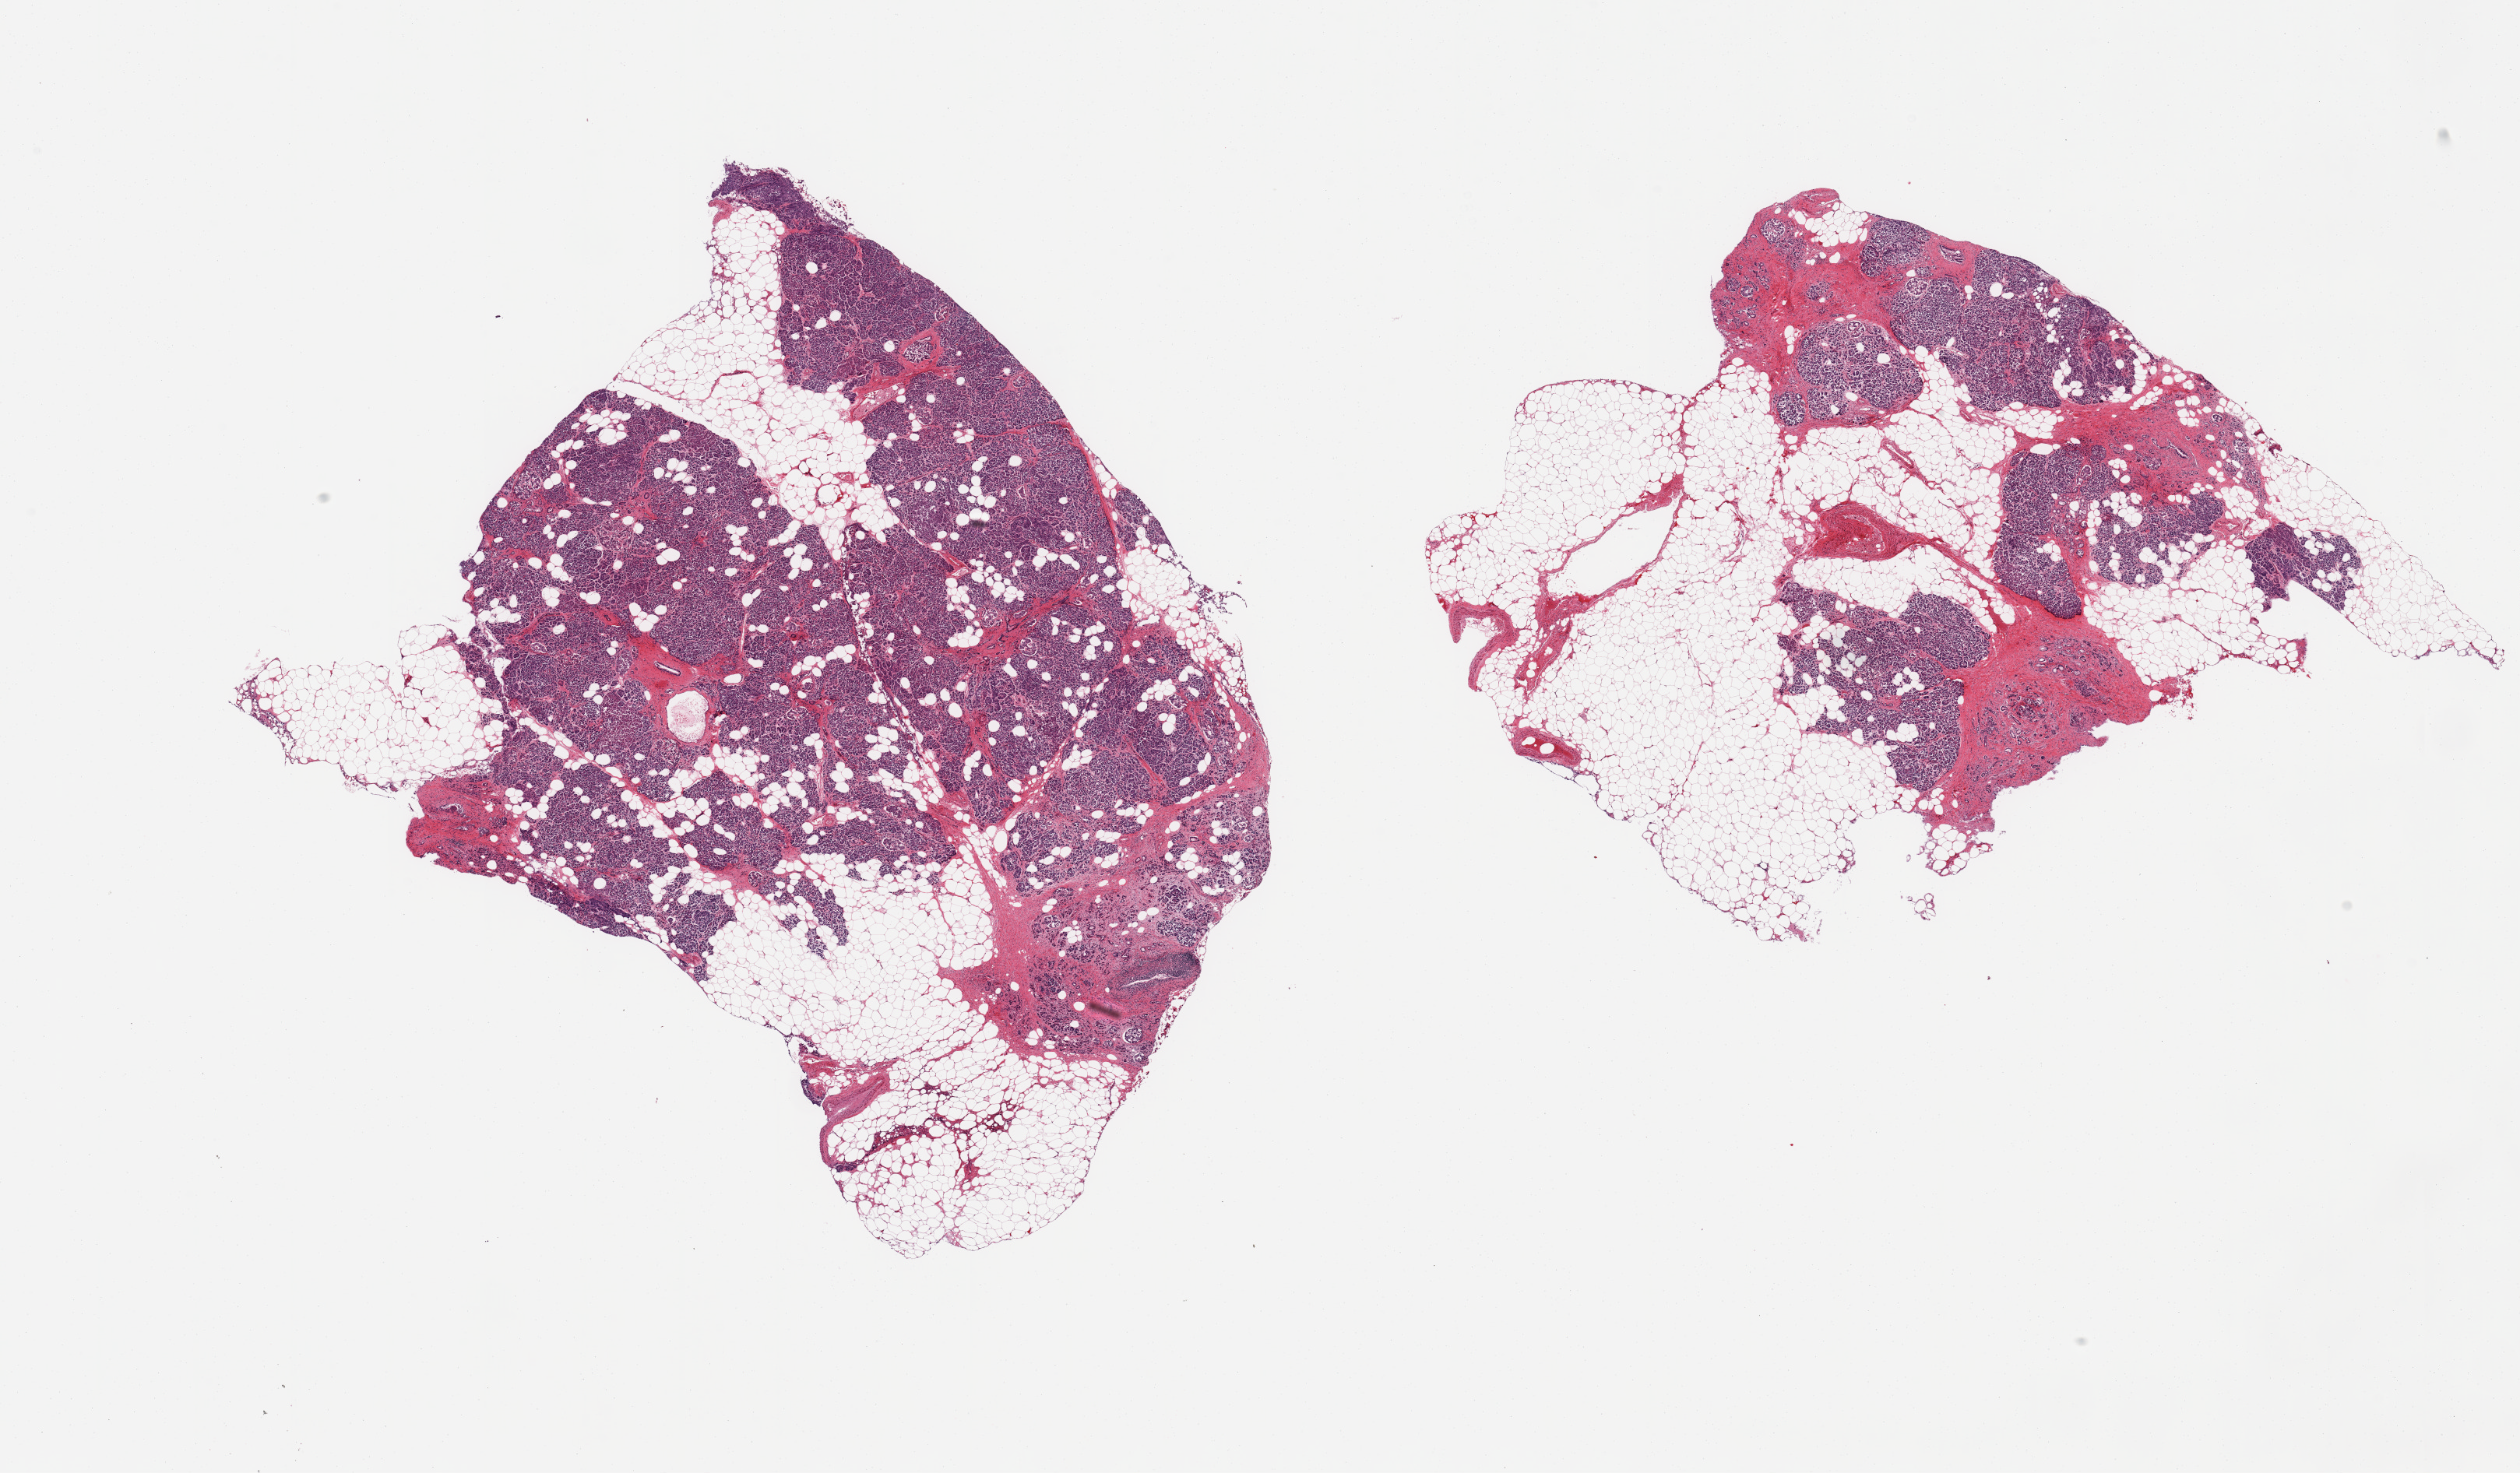
Hematoxylin and eosin (H&E) whole-slide image — a low-resolution overview of the entire scanned area, about 25.6 x 15.0 mm, PAXgene-fixed paraffin-embedded (PFPE) section, section of pancreas (target tissue), donor tissue sample. Donor: male.
Pathologist's review note for this sample: 2 pieces, moderately advance saponification. Islets dimly seen, degeneratiang.